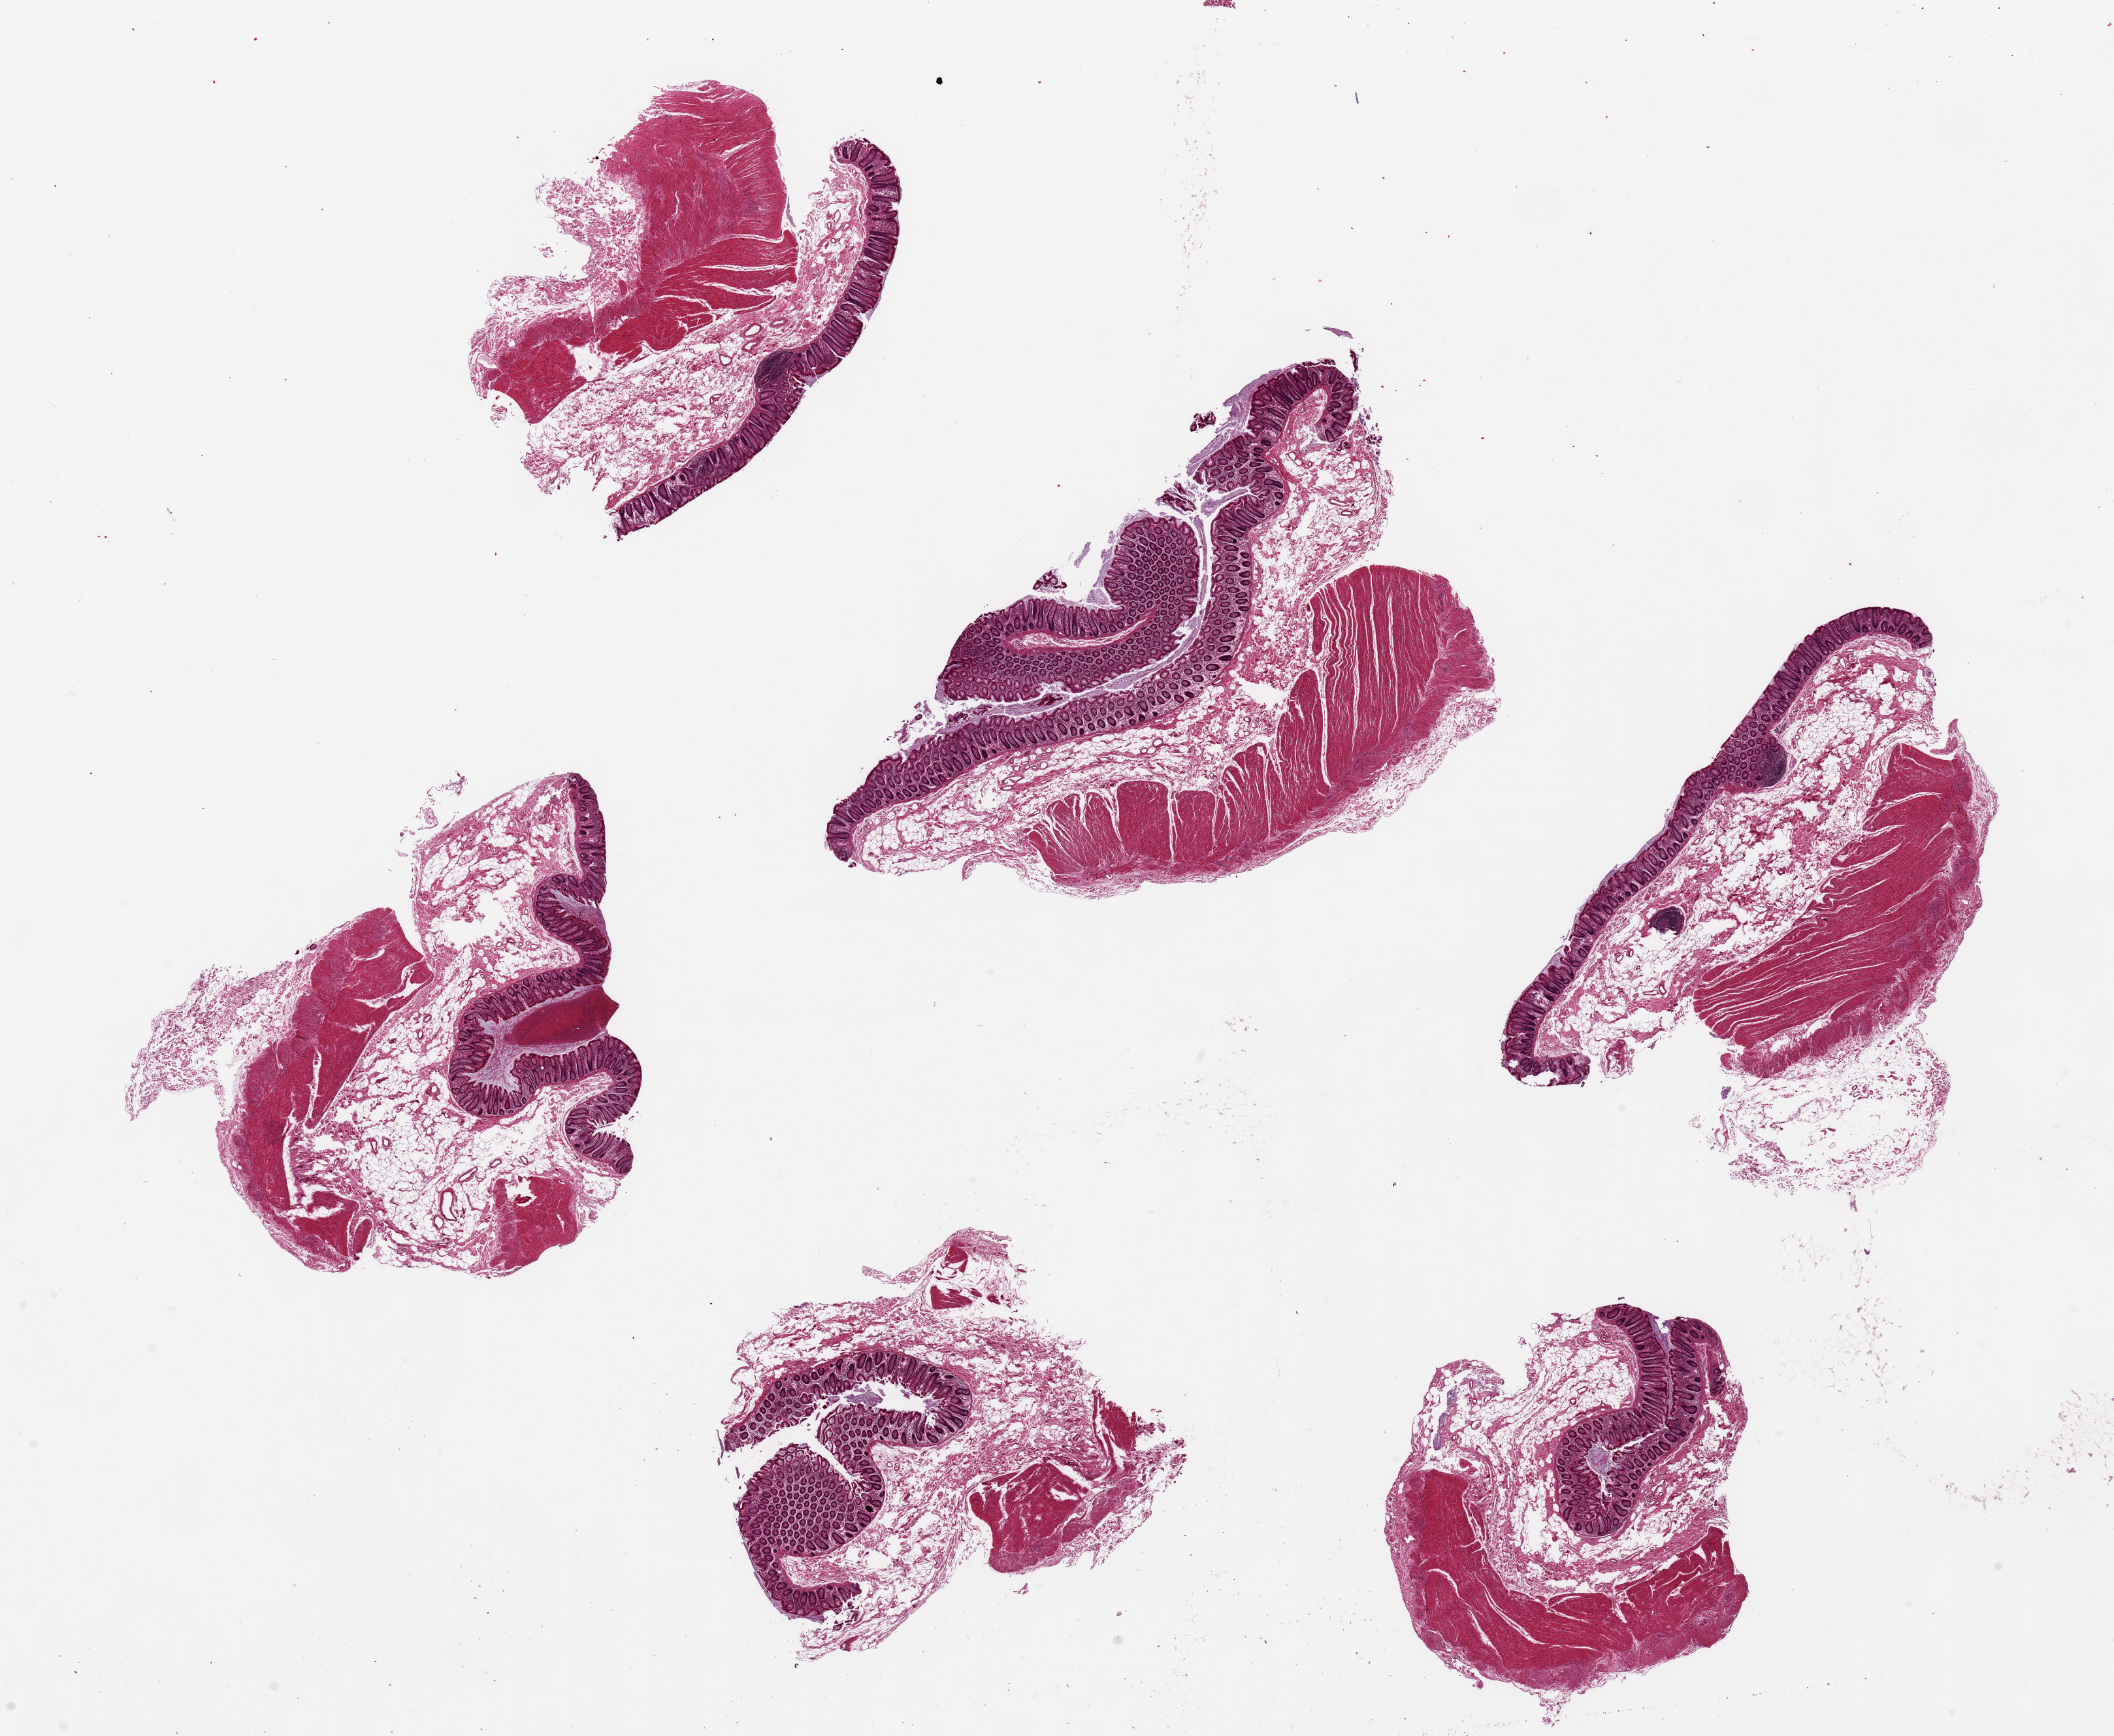
Haematoxylin and eosin whole-slide image, brightfield — low-resolution overview of the scanned area, about 25.6 x 21.0 mm; PAXgene-fixed, paraffin-embedded tissue; sampled site (target tissue): transverse colon; donor tissue sample.
• review note (as recorded): 6 pieces ~7x4mm. Mucosa unusually well-preserved; ~10% of thickness